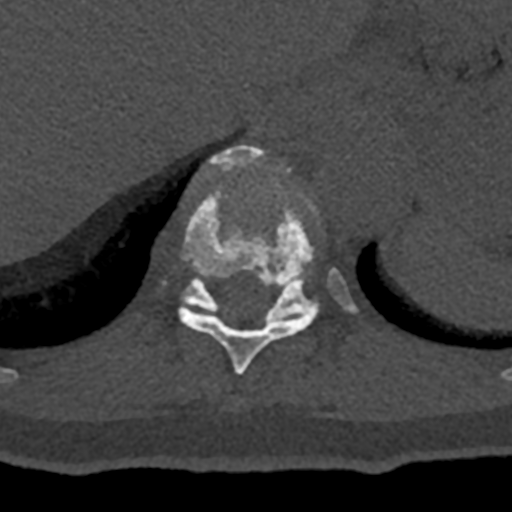
CT including the spine, one axial slice; slice 585 of 797 in the series (ordered by position); bone window (W 1800 / L 400 HU); 0.5 mm slice thickness; 512 × 512 image matrix, field of view 160 × 160 mm. Male patient, age 74 years. From the clinical record (not read from this slice): primary cancer: renal.
Outlined on this slice (semi-automatic segmentation, software-assisted and operator-edited):
- T10 vertebra: bounding box [x1, y1, x2, y2] px = [178, 146, 317, 375]
- T11 vertebra: [163, 267, 357, 320]